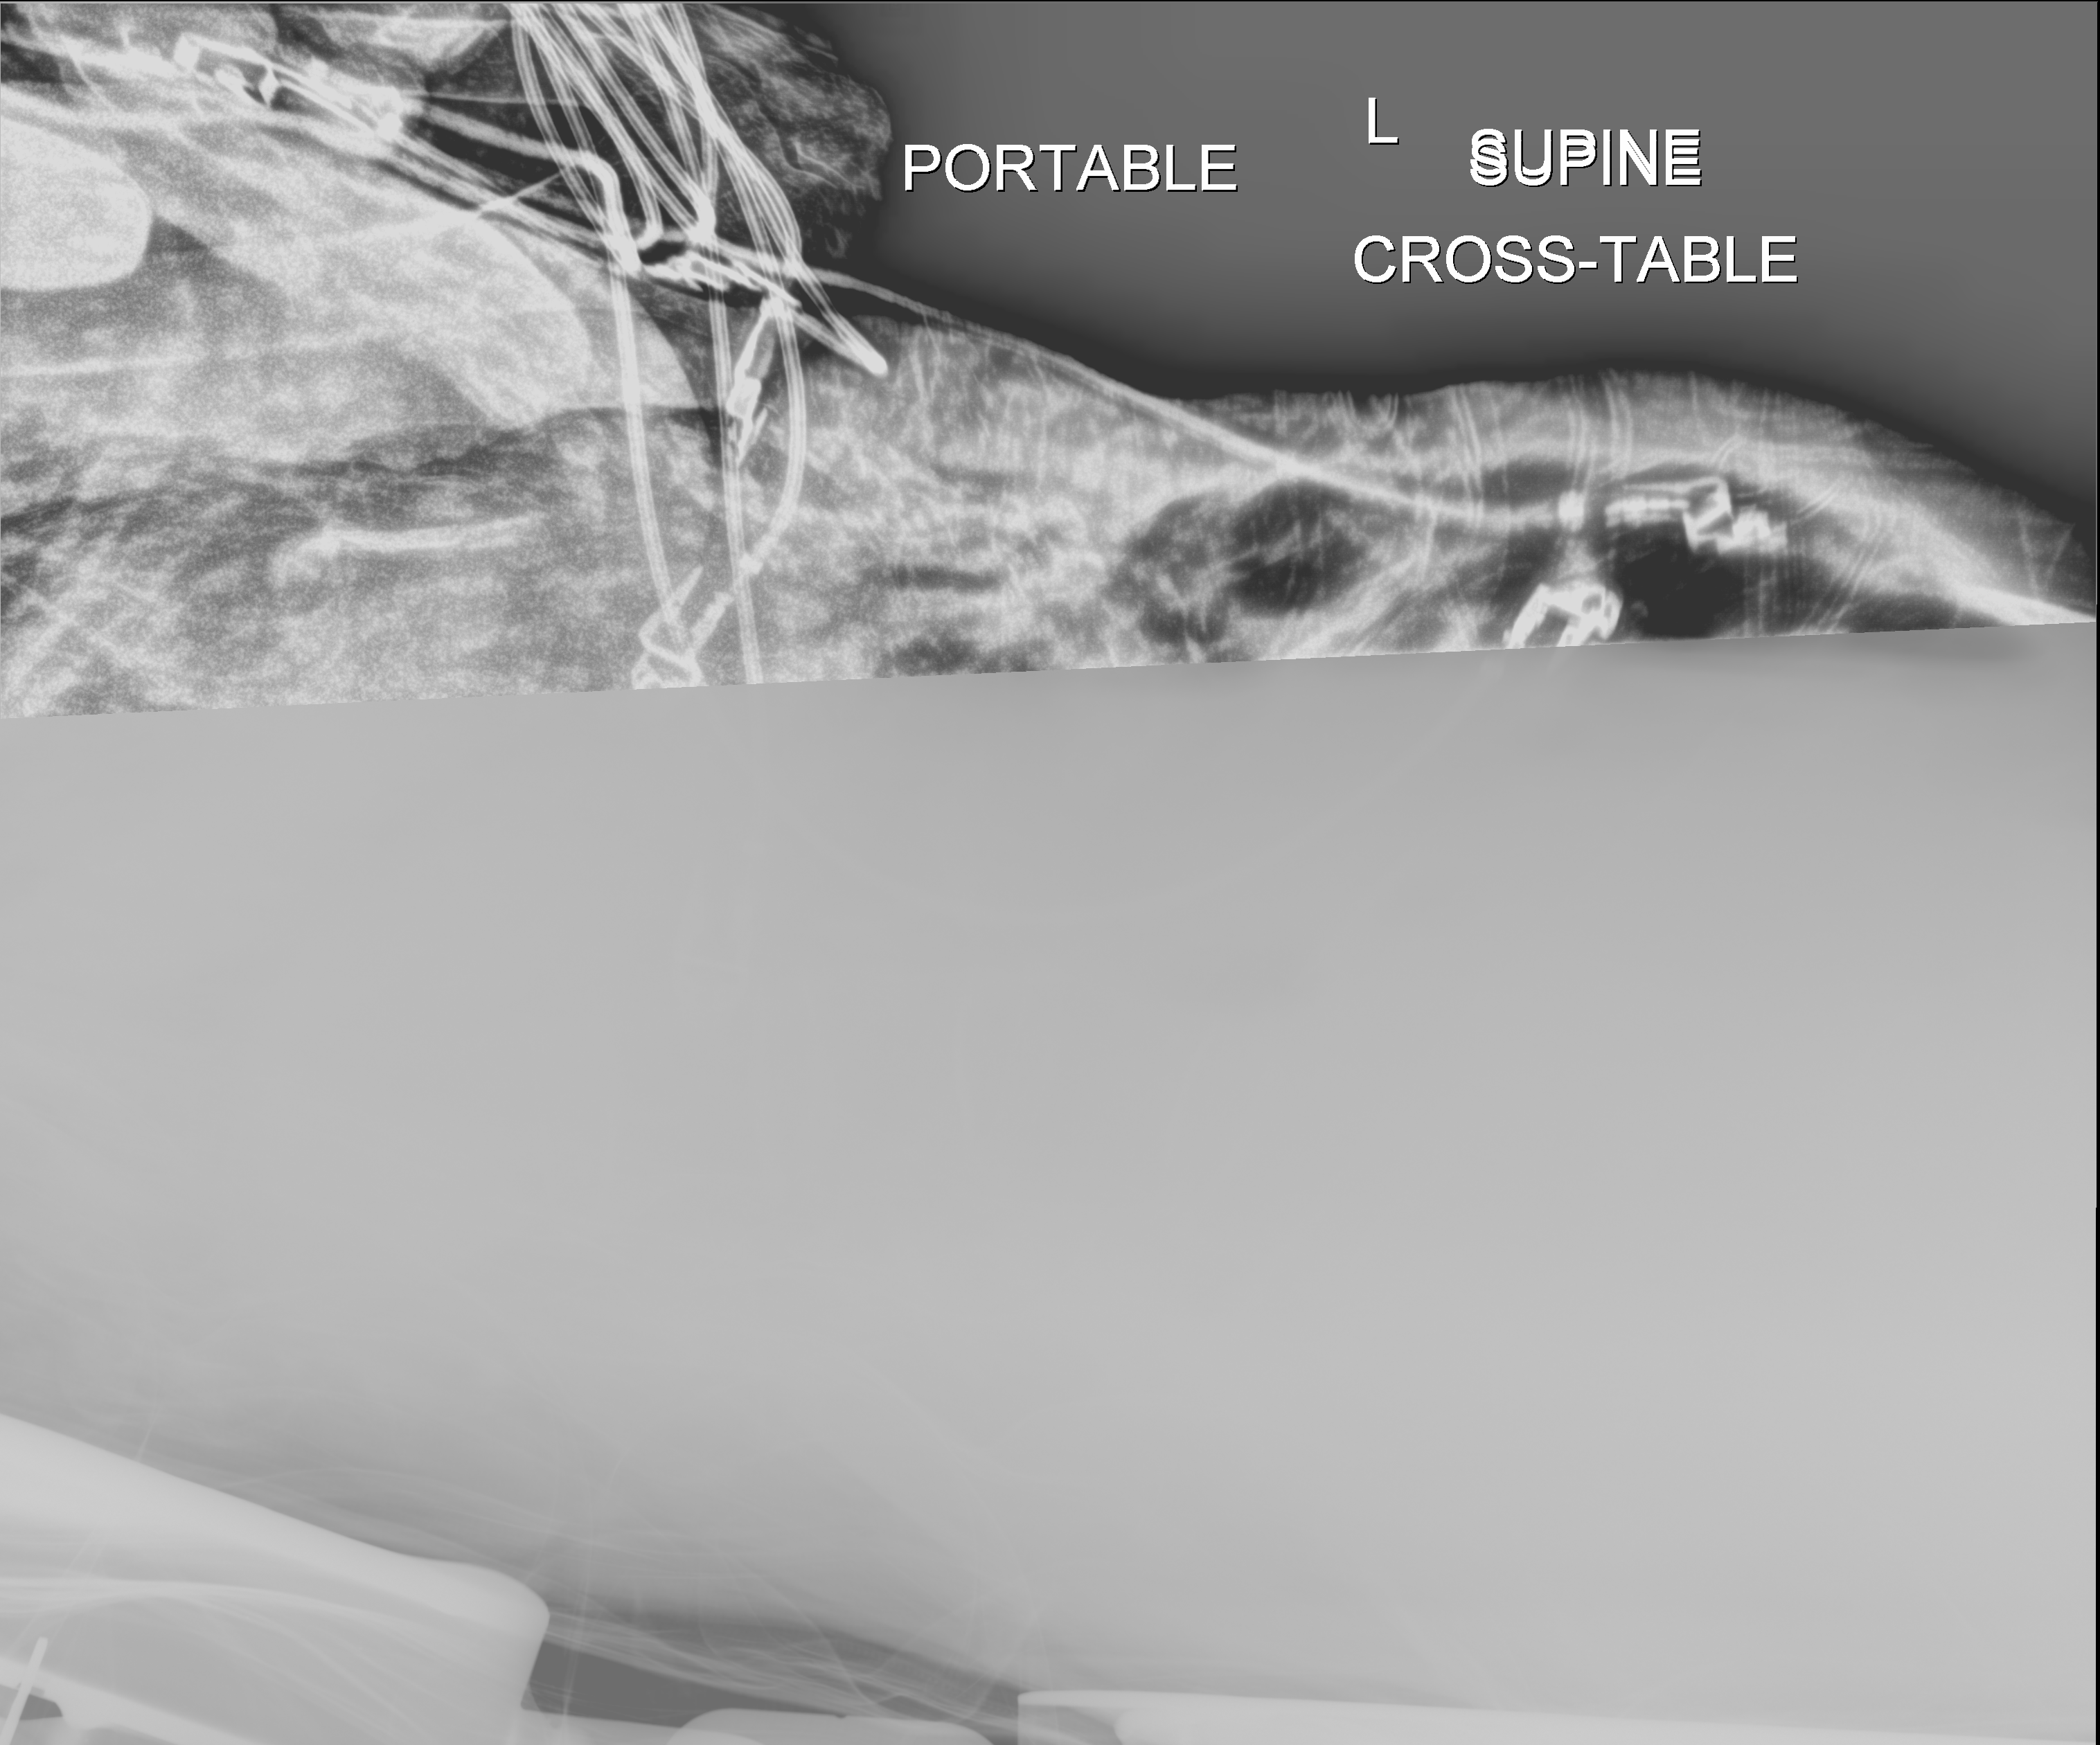
Bedside abdomen radiograph (digital radiography); anteroposterior (AP) projection. Female patient hospitalised with COVID-19, age 75–90 years.
From the hospital-stay record, not from the radiograph (when in the stay this image was taken is not recorded): chronic kidney disease (admission record): no; hypertension (admission record): yes.